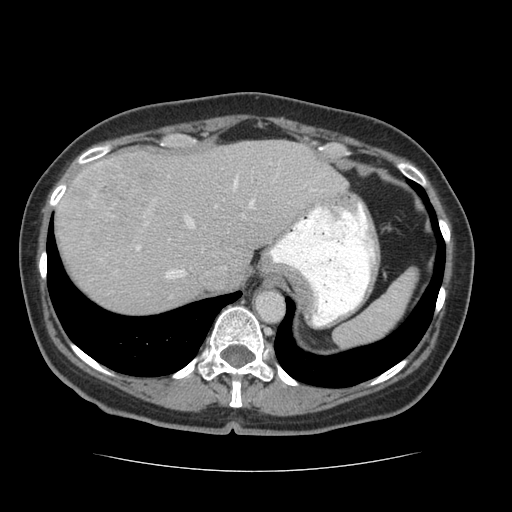
Contrast-enhanced abdominal CT (liver protocol), one axial slice. Position 53 of 75 along the scan axis. Reconstruction kernel STANDARD. 140 kVp. Soft-tissue window (W 400 / L 40 HU). 2.5 mm slice thickness. 512 × 512 image matrix. Case-level facts recorded for this patient, not image findings: diagnosis: hepatocellular carcinoma (patient treated with transarterial chemoembolisation; whether this scan precedes or follows treatment is not stated here); TNM stage (as recorded): Stage-I; Child-Pugh class: A; tumour differentiation: moderately differentiated; tumour nodularity: uninodular.
Structures marked on this image (semi-automatically segmented with operator editing):
- abdominal aorta: bounding box <255,291,285,322> (left, top, right, bottom; pixels)
- liver parenchyma outside the tumour (the mass and vessels are separate outlines, so this box may not span the whole liver): <56,140,348,312>
- mass: <68,154,172,251>
- liver vessels: <136,163,316,279>